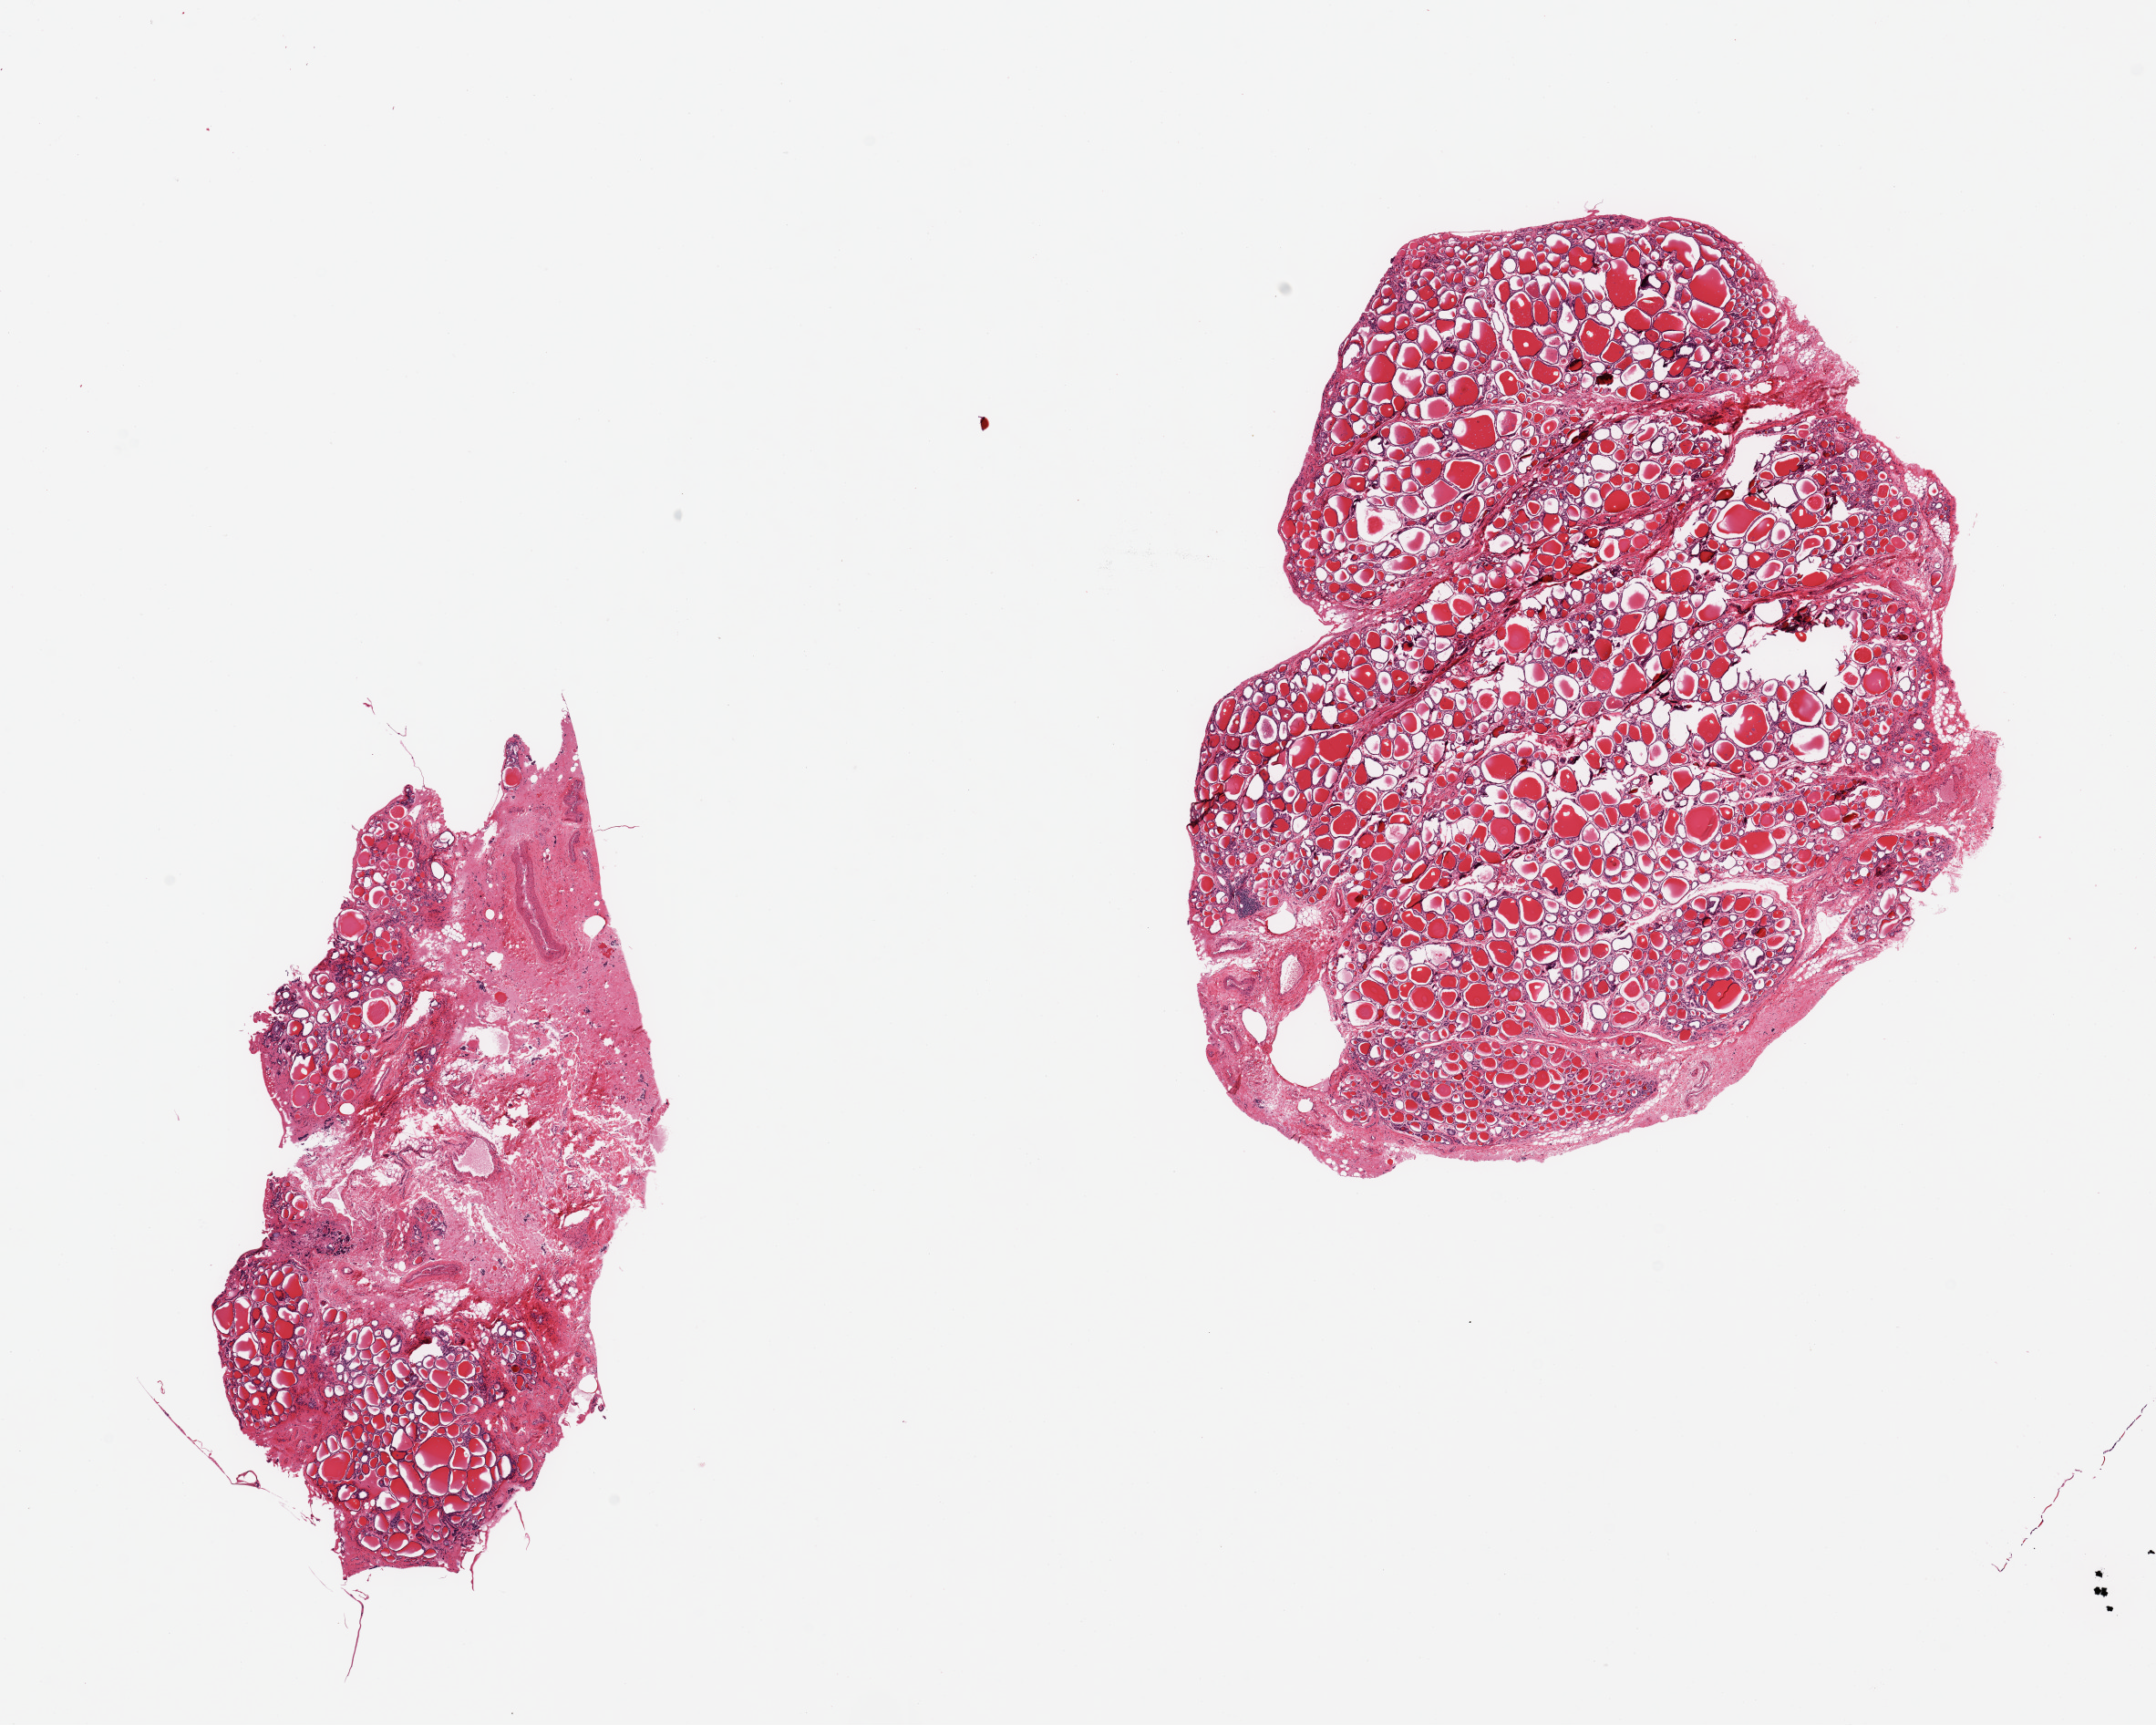
H&E whole-slide image — low-resolution overview of the scanned area, about 18.7 x 15.0 mm (slide scanned at 20x); PAXgene-fixed, paraffin-embedded tissue; section of thyroid (target tissue); tissue donor sample. Donor: female.
* reviewer comment on this tissue sample: 2 pieces, mild nodular goitrous features; ~20% adherent fibrous tissue